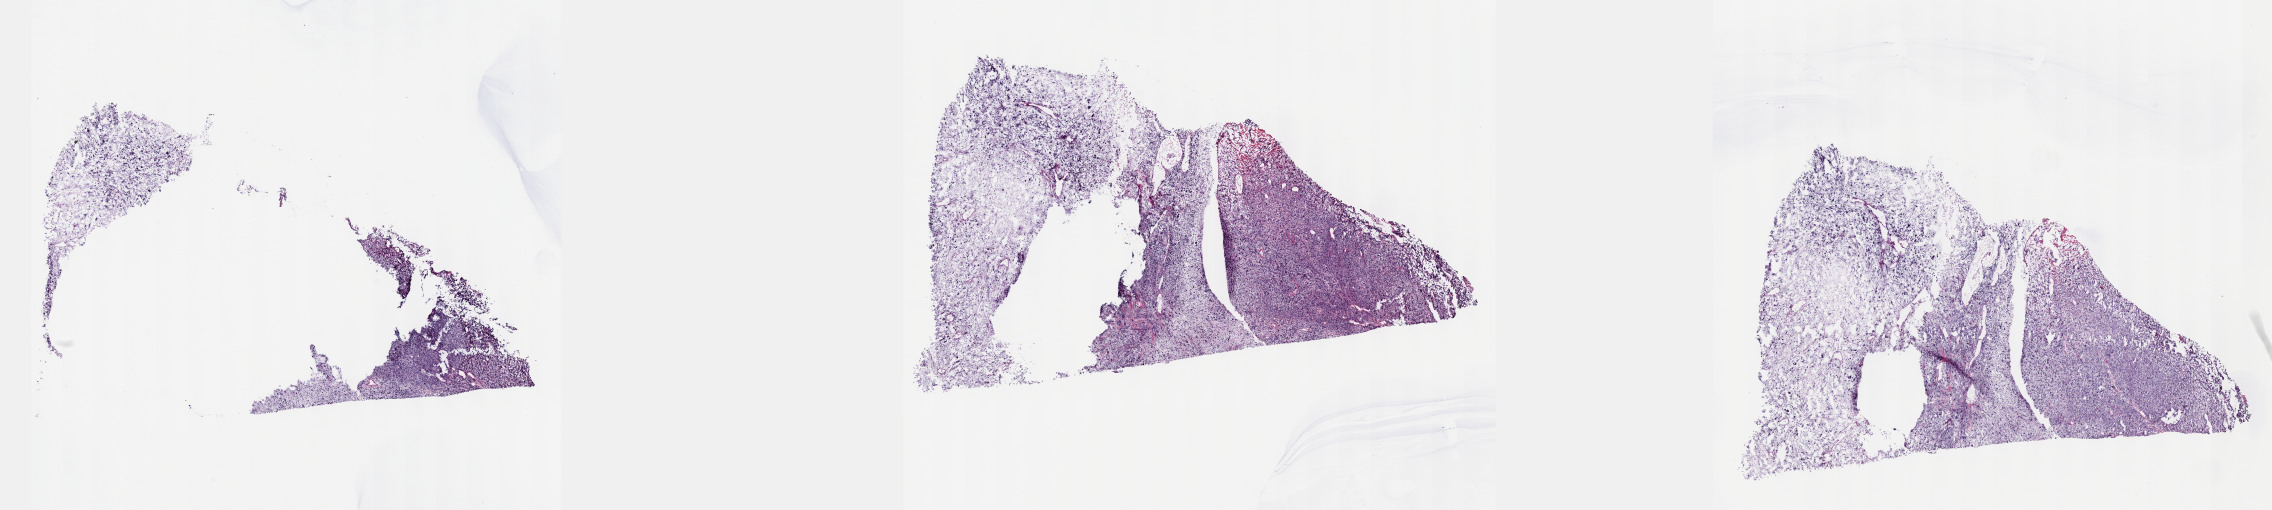
Whole-slide histology image, H&E-stained — whole scanned area (about 36.7 x 8.2 mm) shown as a low-resolution overview. Frozen section from the top of the tissue portion. Primary tumour sample from the connective, subcutaneous and other soft tissues. Female patient; age at initial diagnosis 78 years. Pathologist review of this section (percent, as recorded): tumour cells 100%, tumour nuclei 80%, normal cells 0%, stromal cells 0%, necrosis 0%. Infiltration values recorded for this section: lymphocyte infiltration 2%, monocyte infiltration 0%, neutrophil infiltration 0%.
- pathologic diagnosis: Malignant fibrous histiocytoma (connective, subcutaneous and other soft tissues of lower limb and hip)